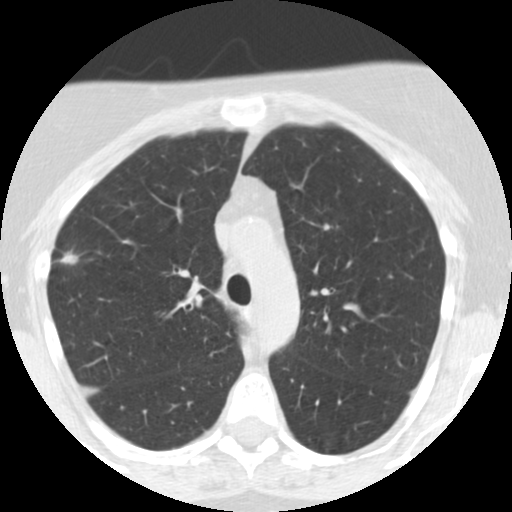
Low-dose screening chest CT, axial slice. Third annual screen. Lung window (W 1500 / L -600 HU). 2.5 mm slice thickness. Slice 178 of 248 in the series. Female, age 55 years at enrolment.
- Expert-annotated lung lesion, bounding box <46,242,90,281> (left, top, right, bottom; pixels).
- Reader record for this screening exam (exam-level; its link to the box is not recorded): non-calcified nodule or mass ≥4 mm, right upper lobe, 10 × 10 mm, poorly defined margins, soft tissue attenuation, pre-existing on the prior screen: yes; interval growth: yes.
- Official screen result: positive, other.
- Lung cancer was diagnosed 145 days after this screen: bronchiolo-alveolar adenocarcinoma, NOS, right upper lobe, moderately differentiated (G2), stage IIA (AJCC 6th edition), 13 mm at pathology.